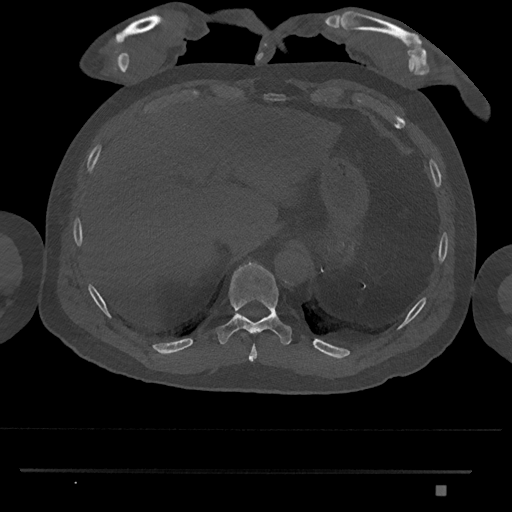
CT including the spine, one axial slice. Slice 1003 of 1134 in the series (ordered by position). Reconstruction kernel Br40s/3. 120 kVp. Bone window (W 1800 / L 400 HU). 0.5 mm slice thickness. 512 × 512 image matrix, field of view 429 × 429 mm. Patient: male, 65 years. From the clinical record (not read from this slice): primary cancer: prostate.
Outlined on this slice (semi-automatically segmented with operator editing):
- T10 vertebra: bounding box [x1, y1, x2, y2] px = [215, 261, 292, 345]
- T9 vertebra: [248, 344, 257, 362]